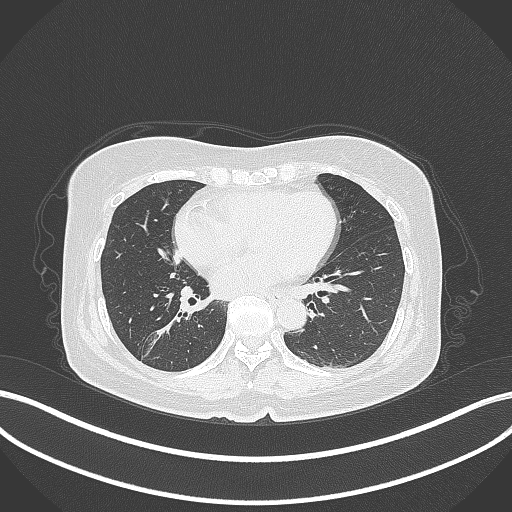
Chest CT, one axial slice; slice 174 of 429 in the series (ordered by position); reconstruction kernel B70f; 120 kVp; lung window (W 1500 / L -600 HU); 1 mm slice thickness; 512 × 512 image matrix. Female patient, age 67 years. Case-level facts recorded for this patient, not image findings: clinical TNM (as recorded): T1c N1 M0; histopathological grade: G2-3.
Outlined on this slice (rectangle marked by the reading radiologist):
- lung tumour (recorded histology: adenocarcinoma): bounding box (x1, y1, x2, y2) in pixels: (146, 297, 198, 341)